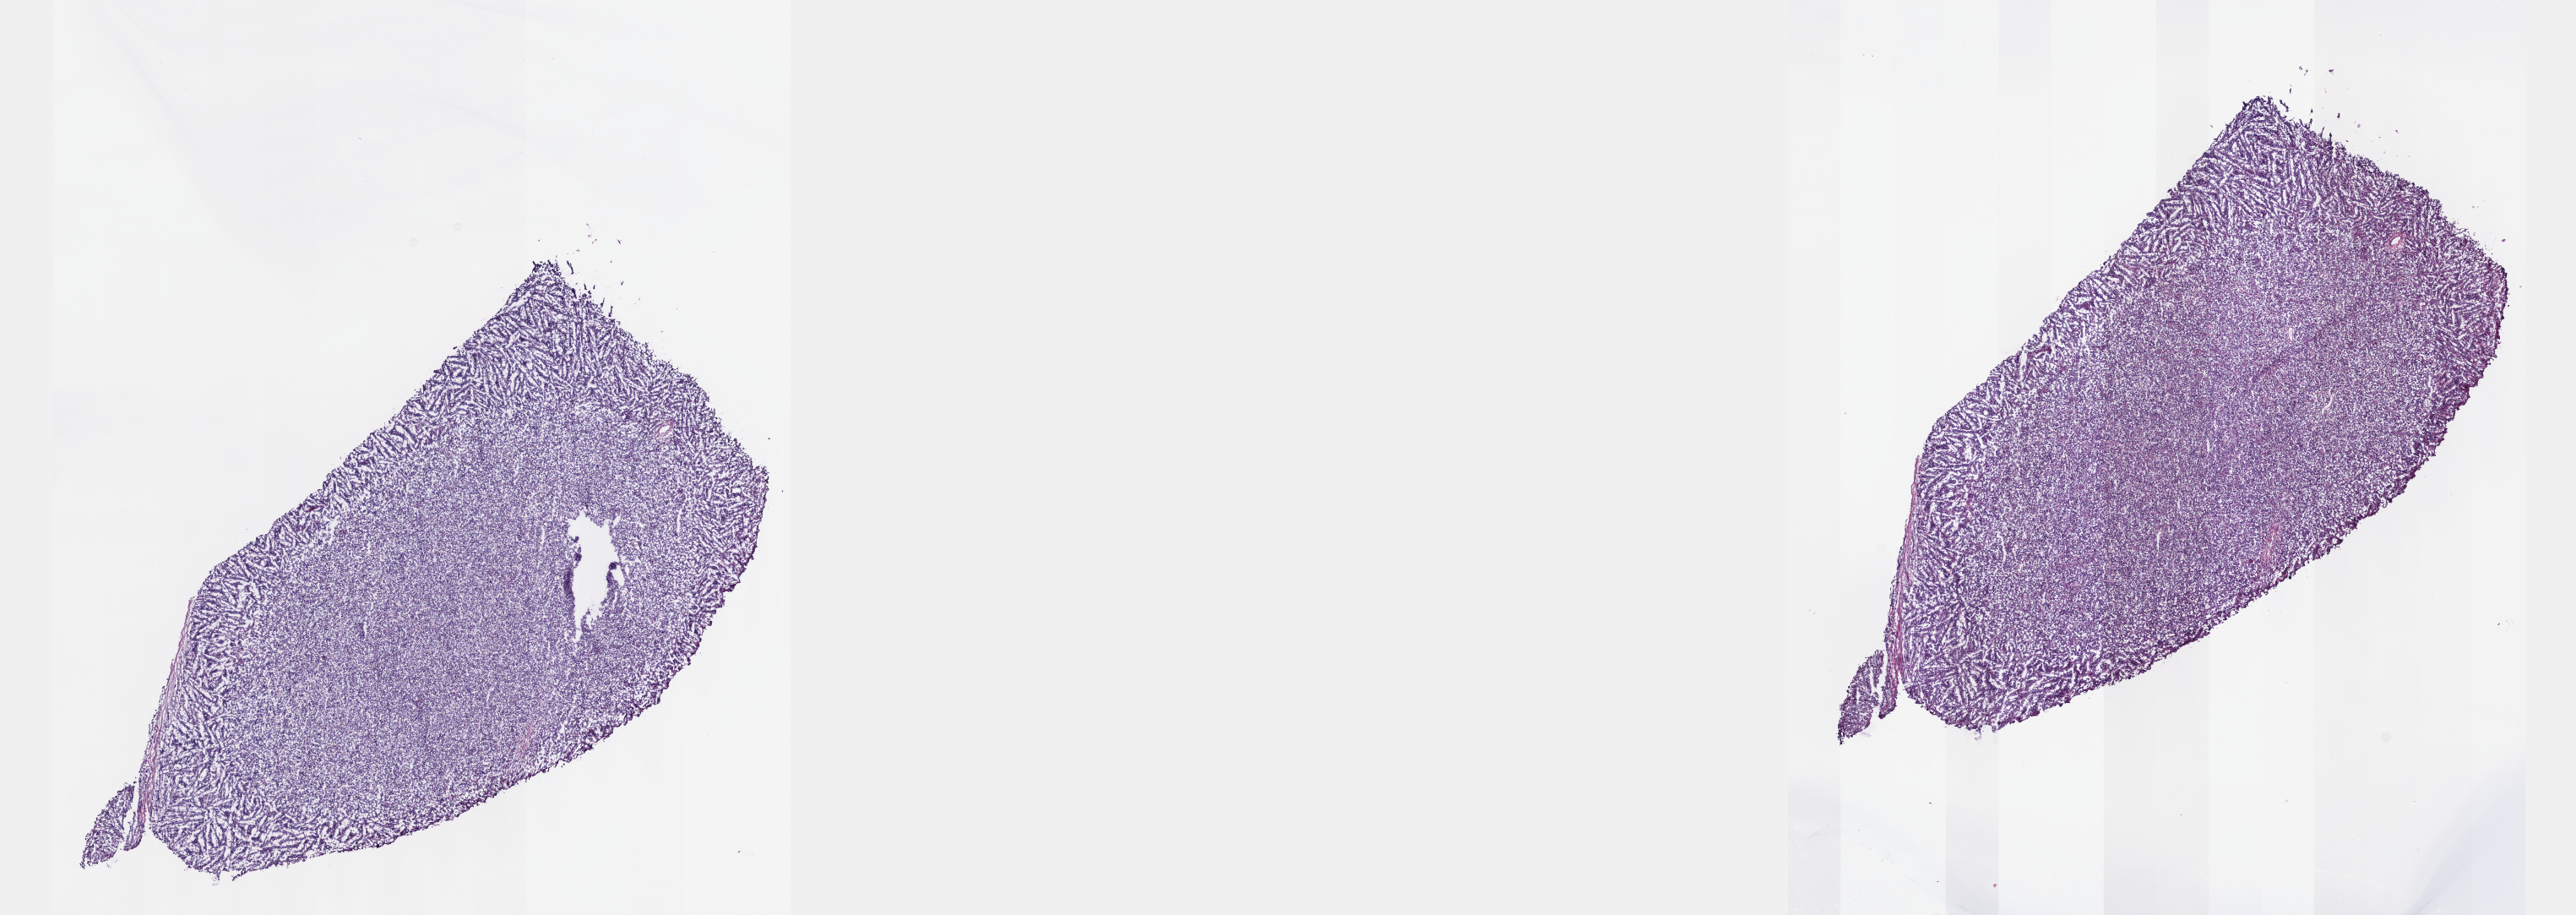
Whole-slide histology image, H&E-stained — whole scanned area (about 24.6 x 8.8 mm, from a 40x scan) shown as a low-resolution overview, frozen section, testis, primary tumour sample. Male patient; age at initial diagnosis 32 years. Composition of this section per pathologist review: tumour cells 100%, tumour nuclei 70%.
Histologic diagnosis: Seminoma, NOS.